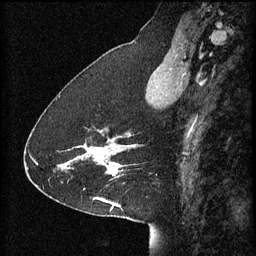
Breast MRI (dynamic contrast-enhanced), one sagittal slice. Slice 24 of 60 in the series (ordered by position). 3 images stored at this slice position (order not interpretable as contrast timing). 1.5 T. TE 4.2 ms, TR 8.2 ms. 2 mm slice thickness. 256 × 256 image matrix, field of view 200 × 200 mm. Female patient, age 41 years.
Outlined on this slice (semi-automatic segmentation, software-assisted and operator-edited):
- analysis volume of interest (the breast-tissue region the enhancement analysis was run in; not a lesion): bounding box <59,138,128,179> (left, top, right, bottom; pixels)
- tumour enhancement mask (voxels above the 70 % enhancement threshold inside the analysis volume of interest): <59,138,128,177>